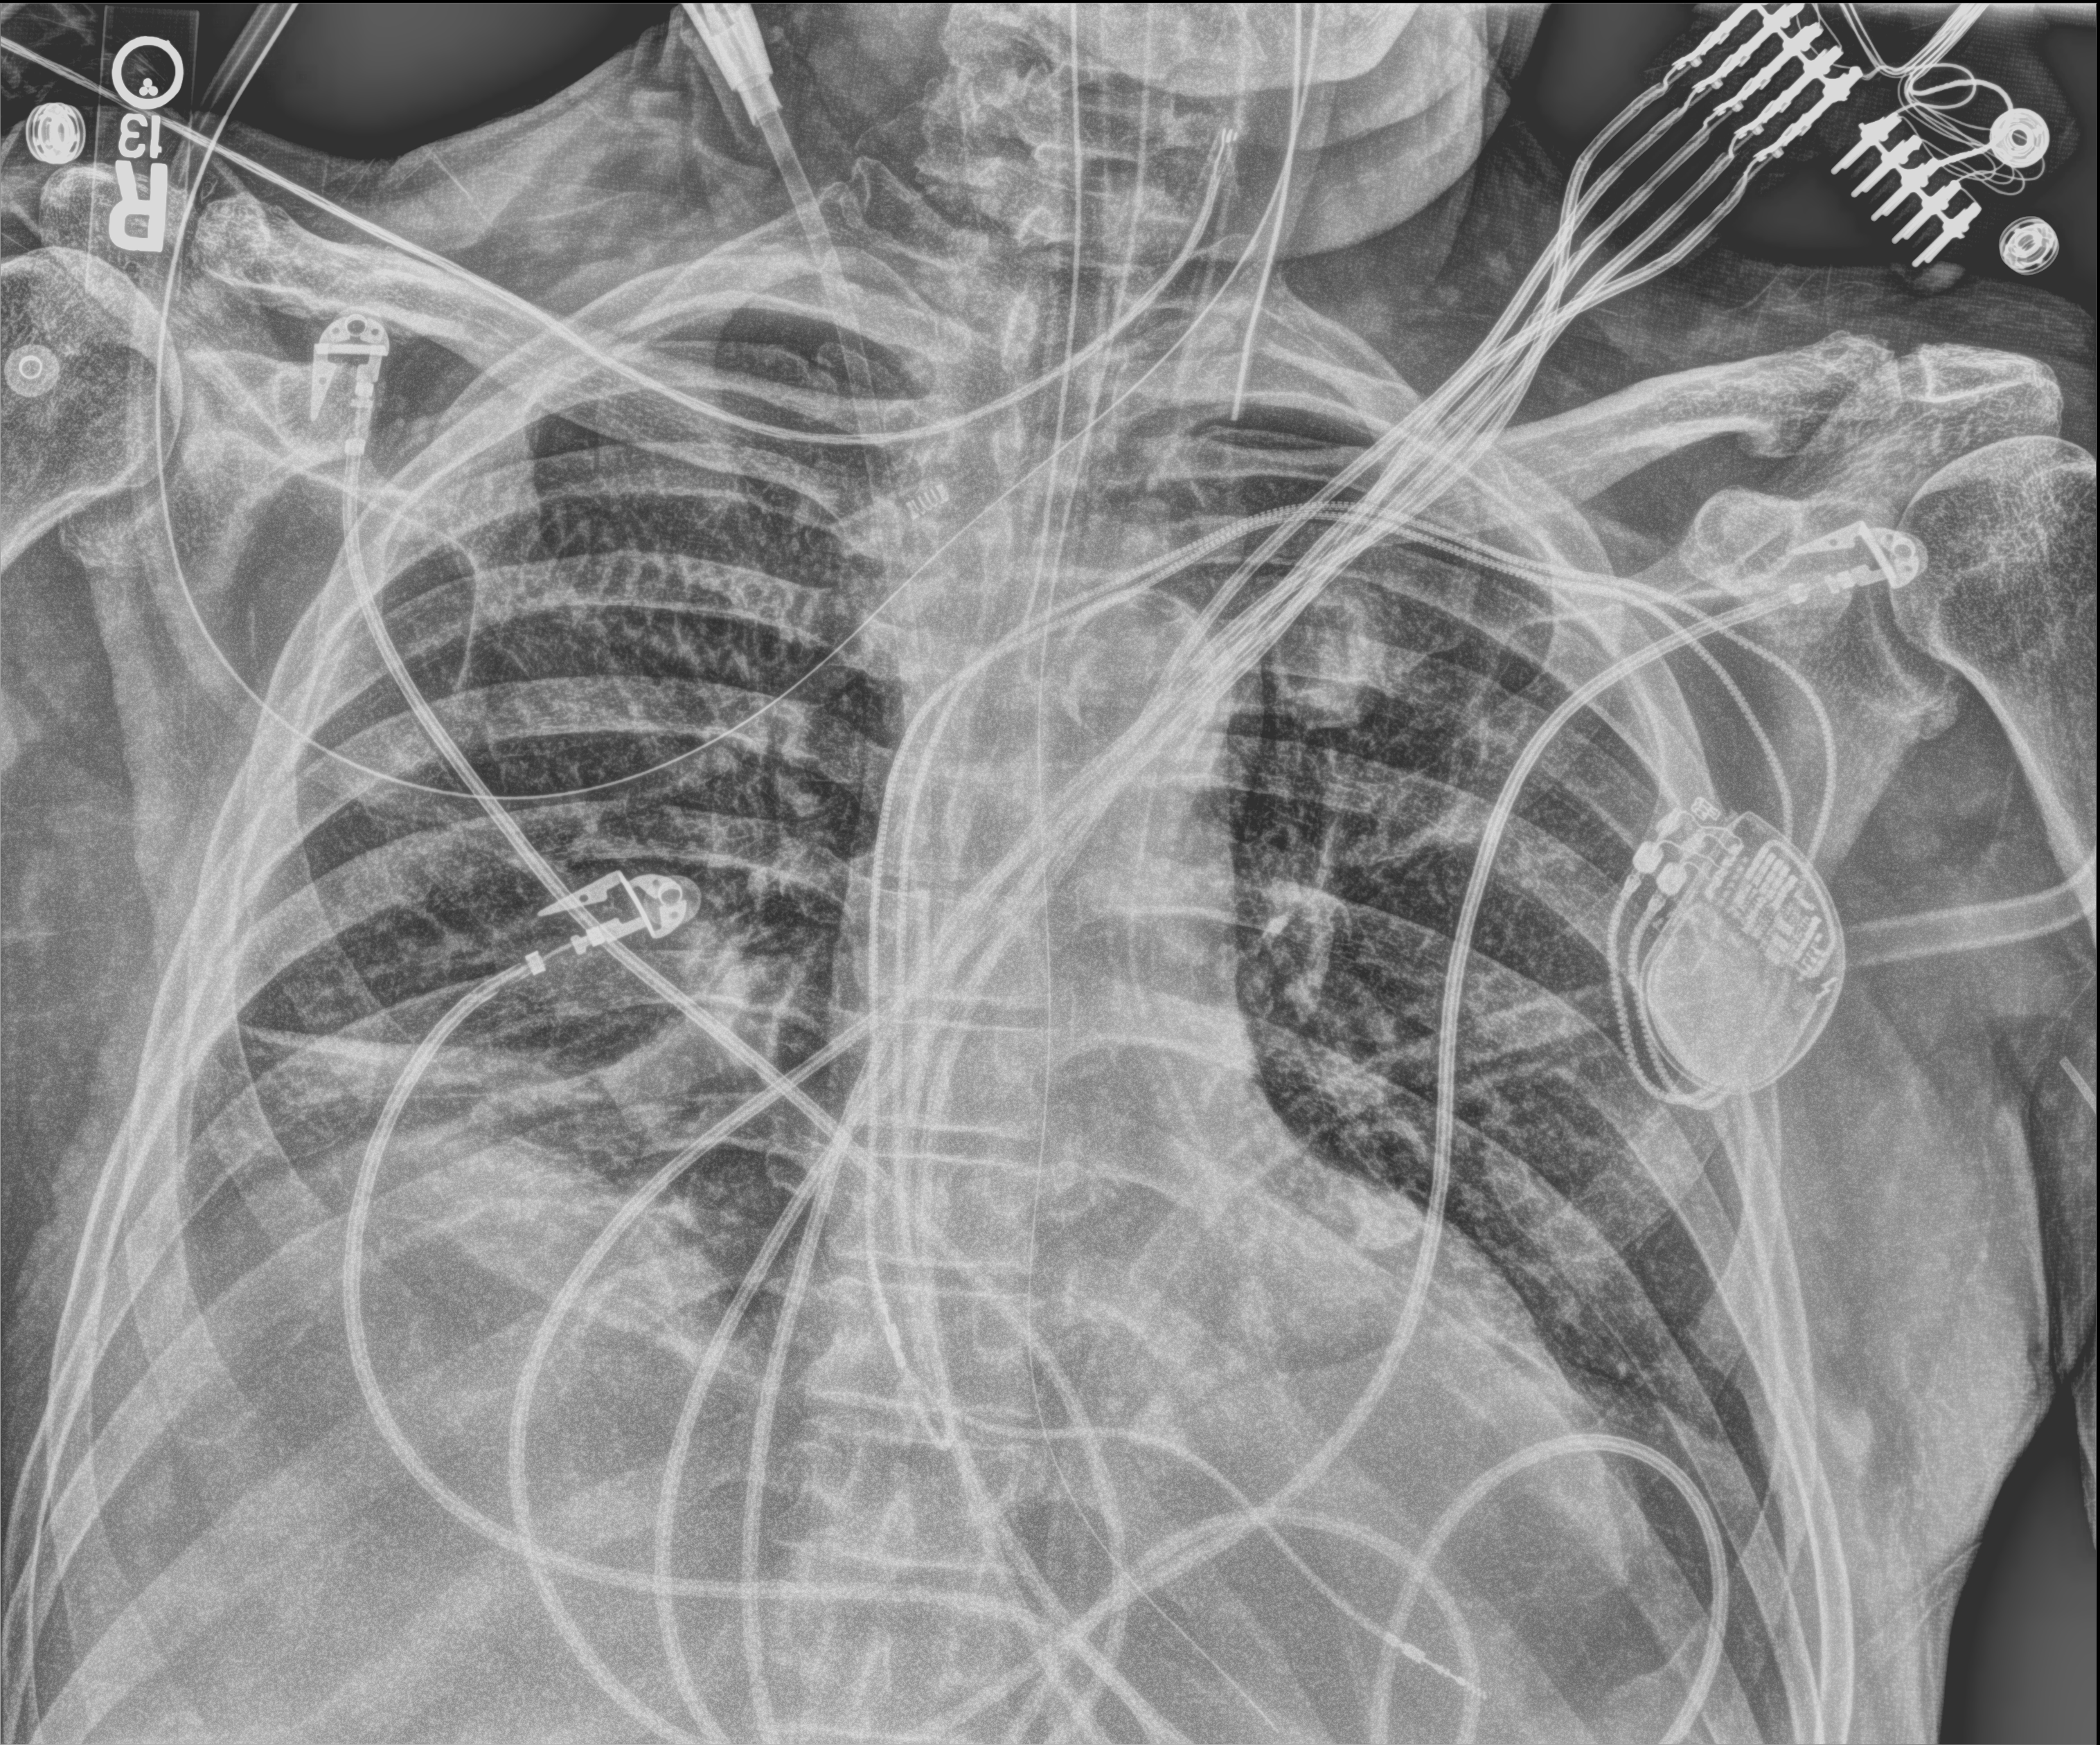
Portable chest radiograph, anteroposterior (AP) projection. Male patient hospitalised with COVID-19, age 60–74 years.
From the hospital-stay record, not from the radiograph (when in the stay this image was taken is not recorded):
- mechanically ventilated during this hospital stay: yes
- admitted to intensive care during this hospital stay: yes